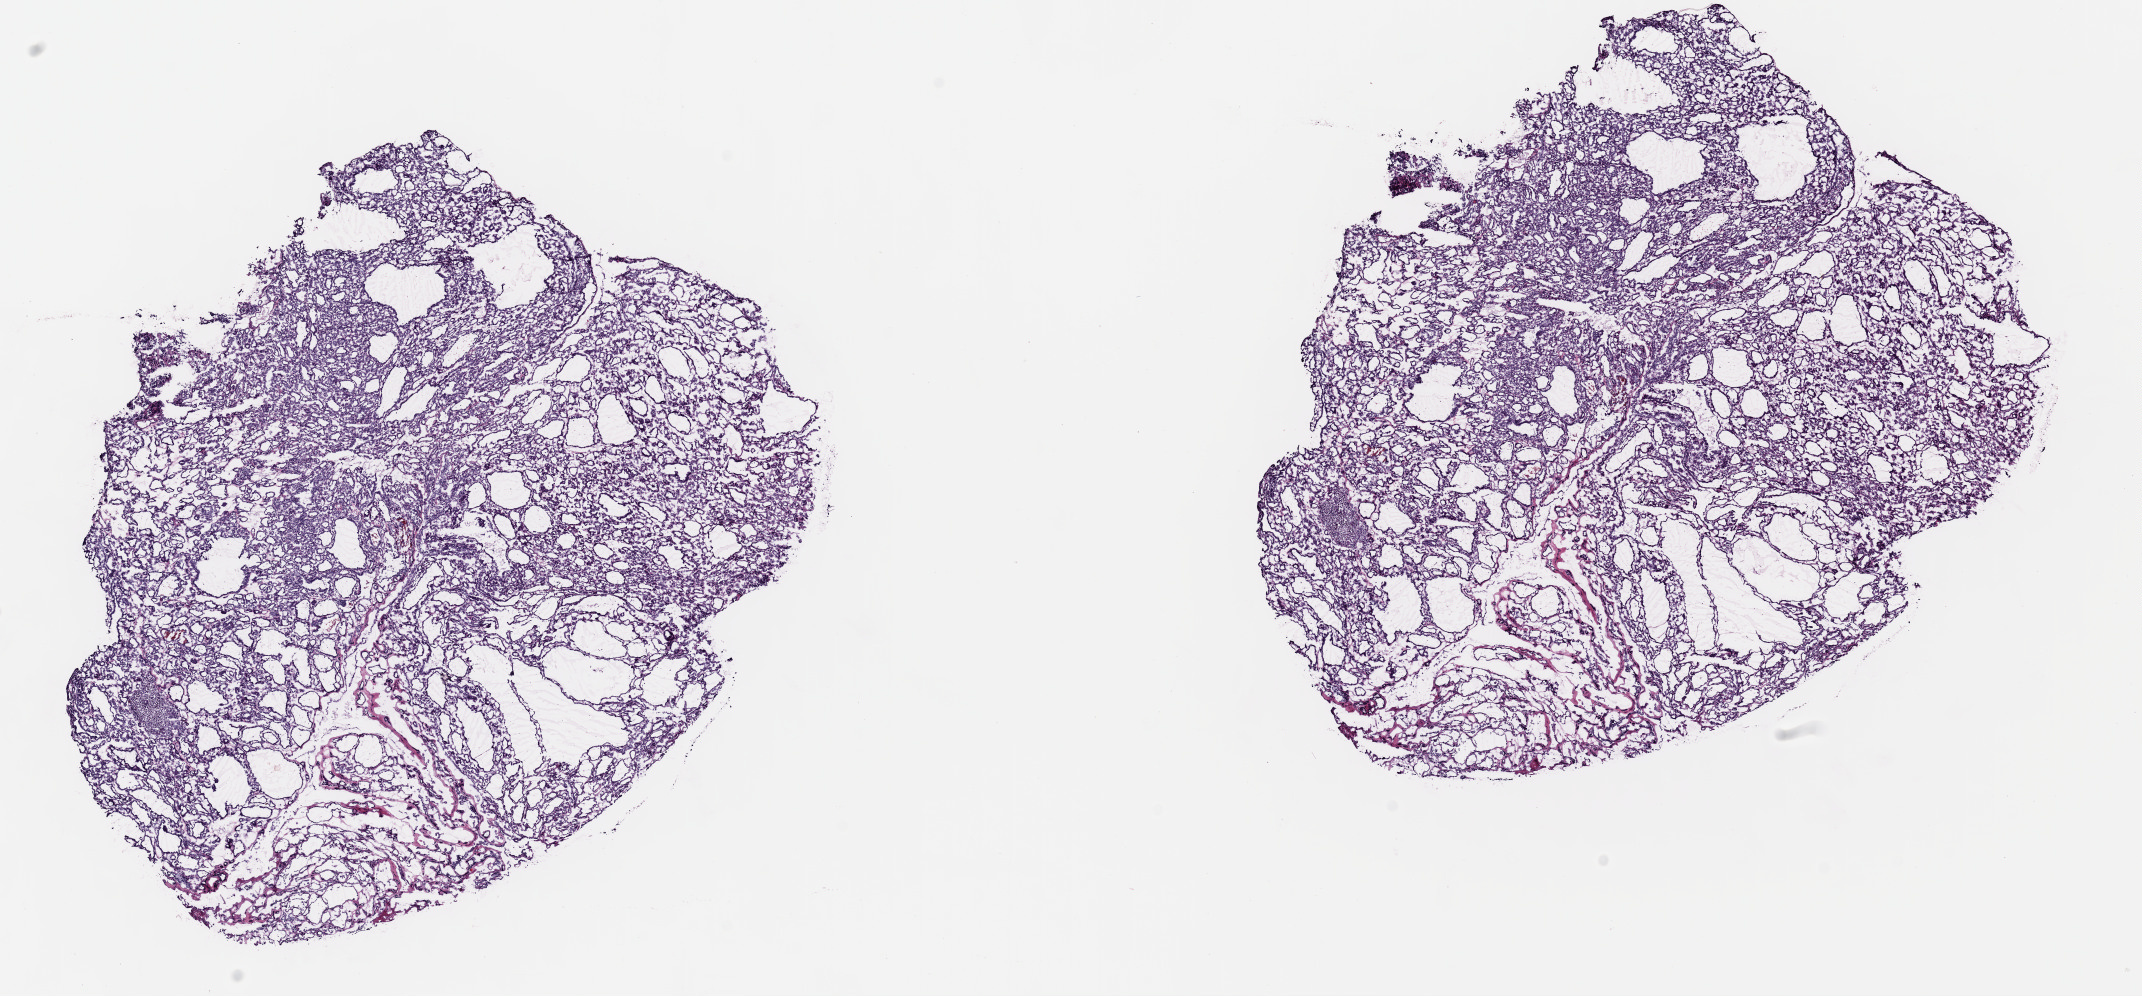
Whole-slide histology image, H&E — a low-resolution overview of the entire scanned area, about 16.9 x 7.9 mm (from a 40x scan), frozen section from the top of the tissue portion, sample: primary tumour, thyroid. Patient: male, age at initial diagnosis 31 years.
Histologic diagnosis: Papillary carcinoma, follicular variant (thyroid gland).